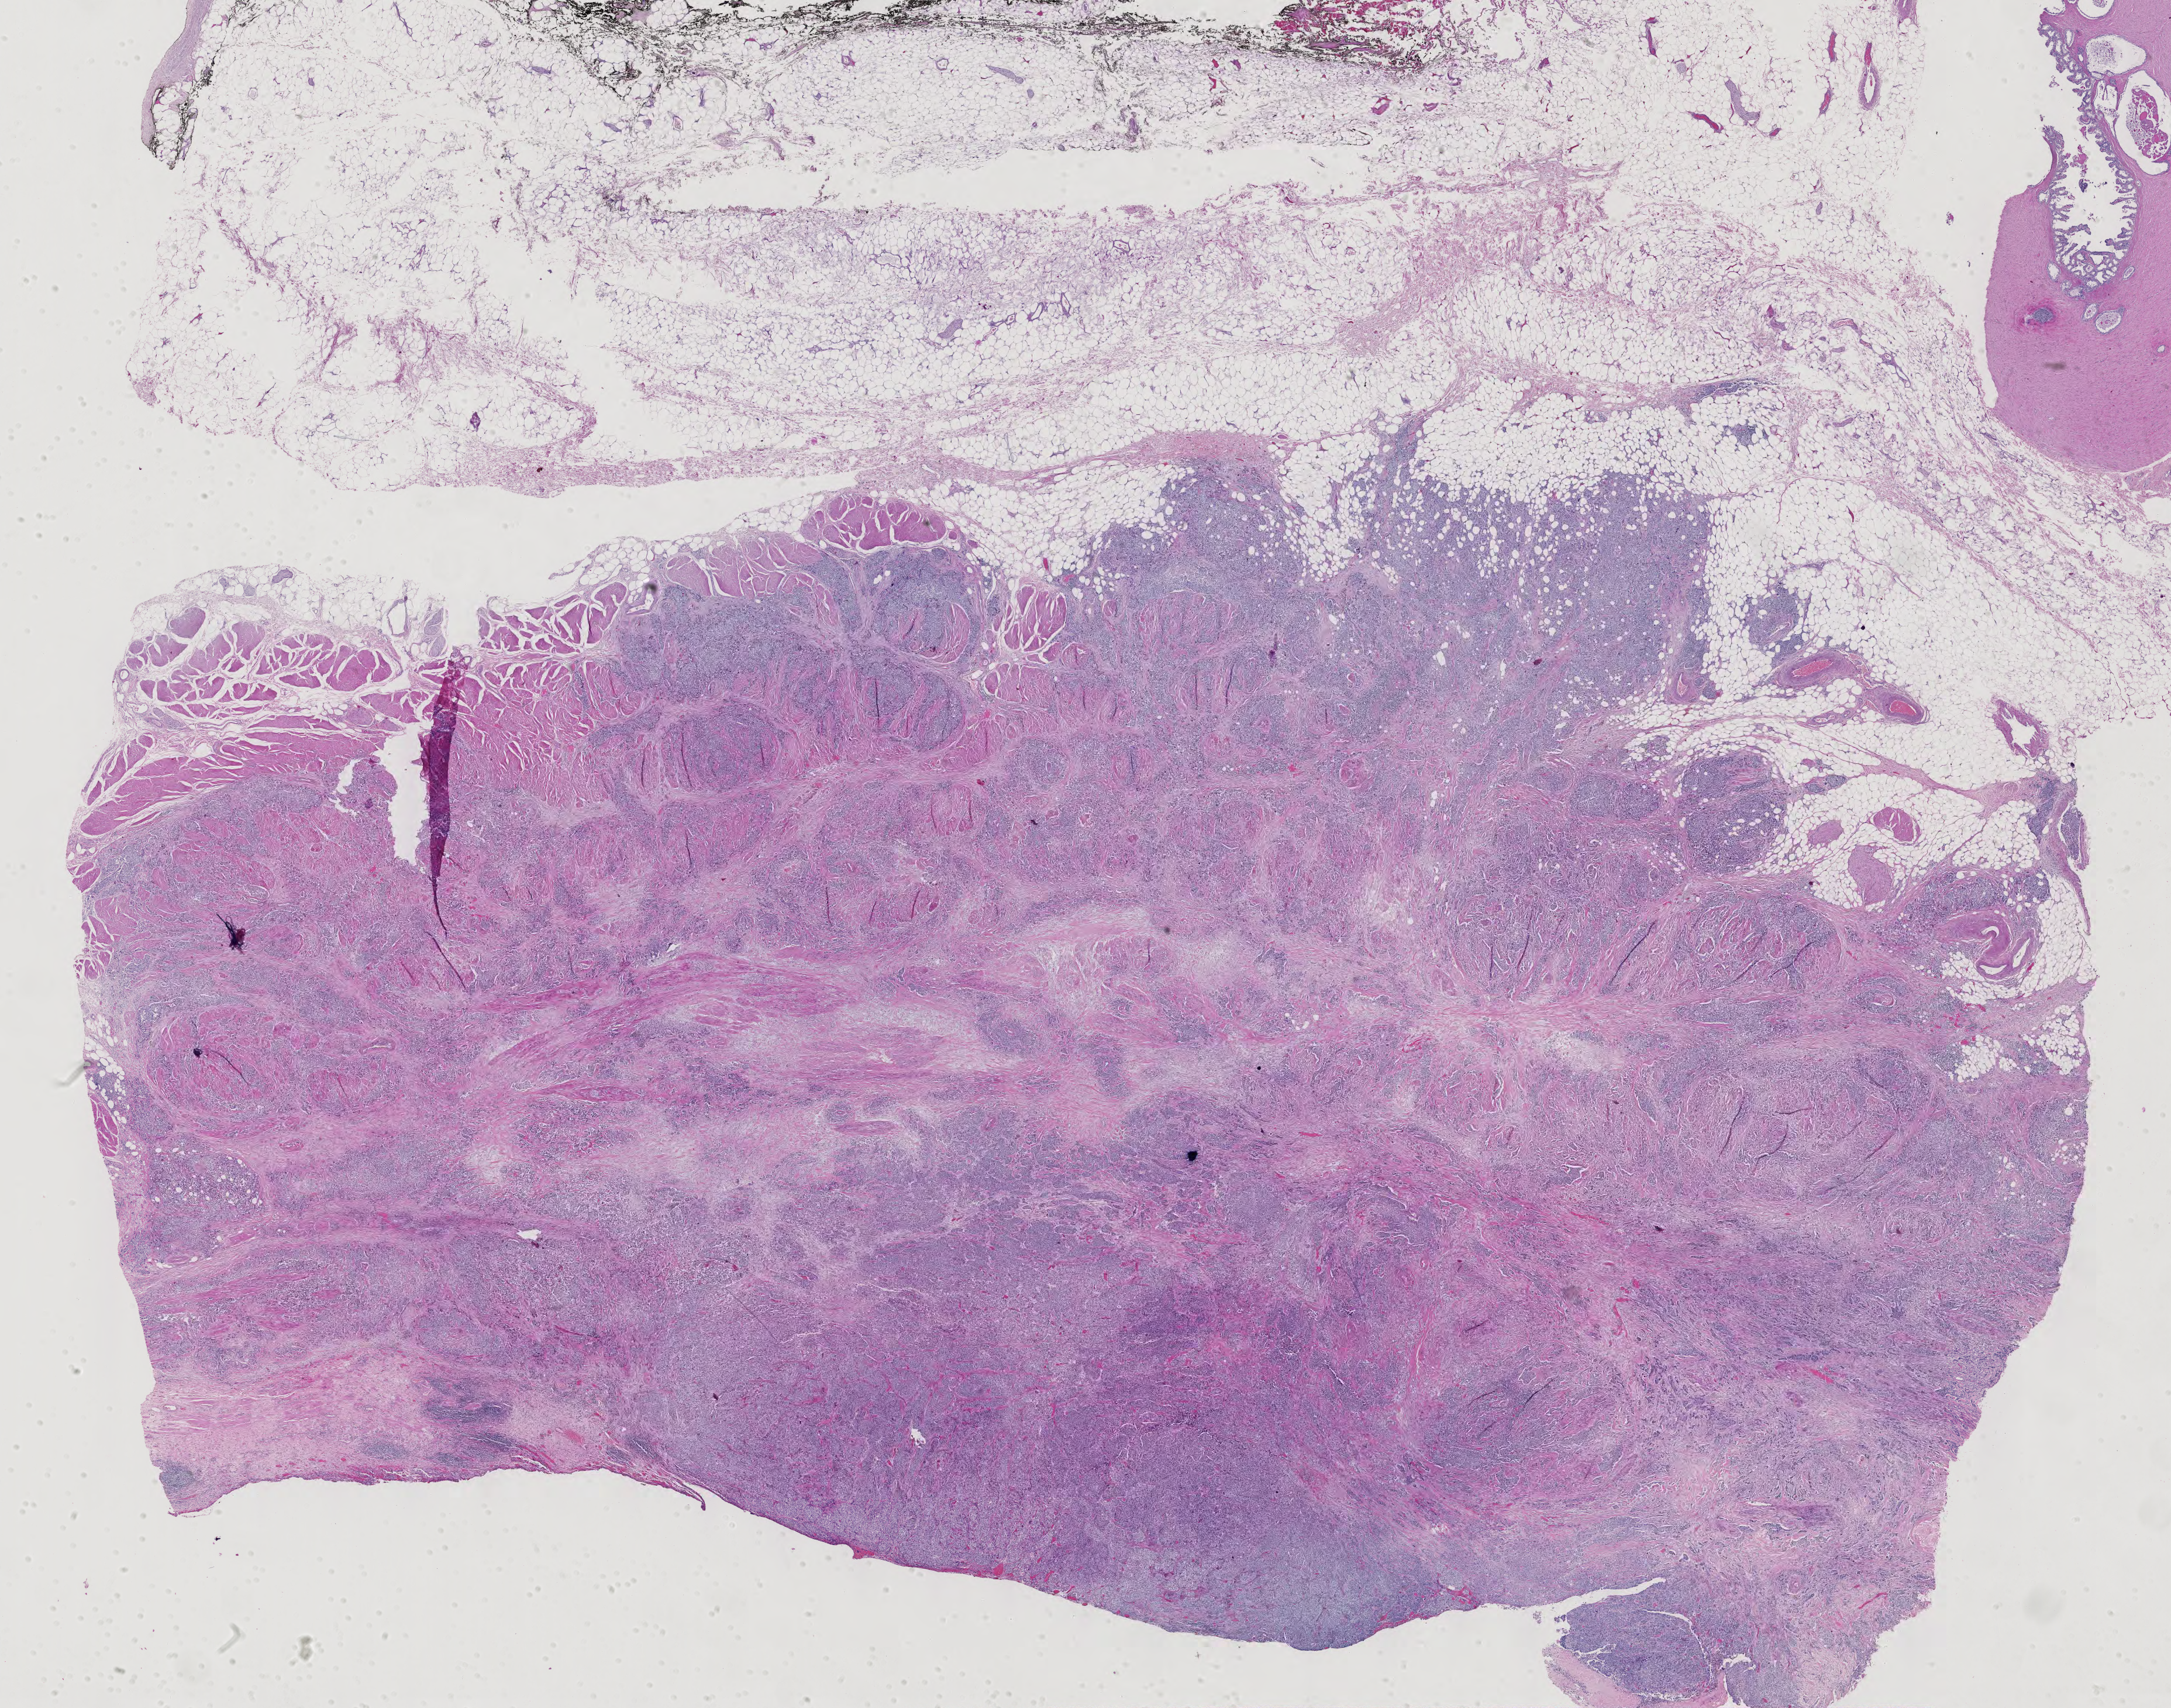
Digitized H&E-stained tissue section (whole slide), a low-resolution overview of the entire scanned area, about 27.0 x 21.3 mm (slide scanned at 40x); FFPE section; sample: primary tumour, bladder. Male patient; age at initial diagnosis 66 years. Histologic grade: high grade.
AJCC pathologic stage: IV. Diagnosis: Transitional cell carcinoma (lateral wall of bladder). Lymph nodes positive (case pathology): 2 of 21 examined.